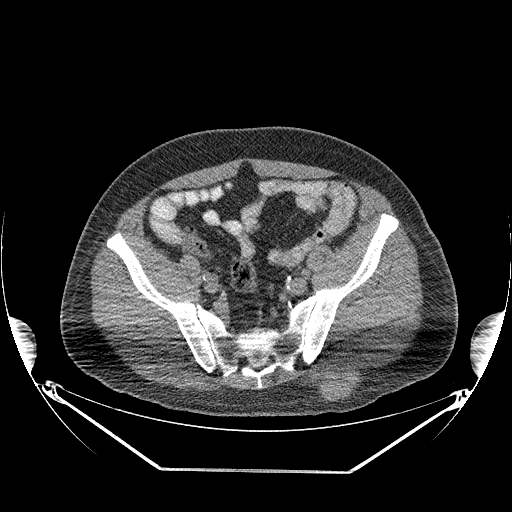
CT of an extremity soft-tissue mass (from a PET/CT study), one axial slice; position 82 of 267 along the scan axis; reconstruction kernel STANDARD; soft-tissue window (W 400 / L 40 HU); 512 × 512 image matrix, field of view 500 × 500 mm. Male patient. Case-level facts recorded for this patient, not image findings: histological type: pleiomorphic leiomyosarcoma; grade: high; site of the primary tumour: left buttock.
Annotated regions visible in this slice (expert contour drawn on MRI and transferred to this co-registered scan by the dataset authors):
- gross tumour volume including surrounding oedema: bounding box <320,375,357,401> (left, top, right, bottom; pixels)
- gross tumour volume (mass): <326,380,355,400>